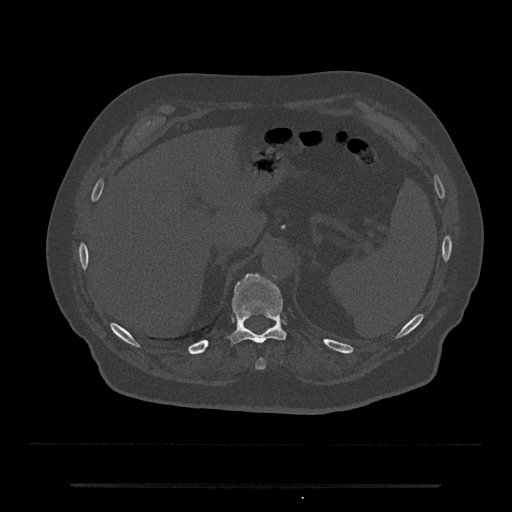
CT including the spine, one axial slice; position 652 of 797 along the scan axis; reconstruction kernel Br40s/3; bone window (W 1800 / L 400 HU); 512 × 512 image matrix. Male patient, age 80 years. From the clinical record (not read from this slice): primary cancer: prostate; vertebrae with lytic lesions (as recorded): L1, T11.
Annotated regions visible in this slice (semi-automatic segmentation, software-assisted and operator-edited):
- T10 vertebra: bounding box (x1, y1, x2, y2) in pixels: (256, 358, 265, 370)
- T11 vertebra: (230, 274, 286, 344)